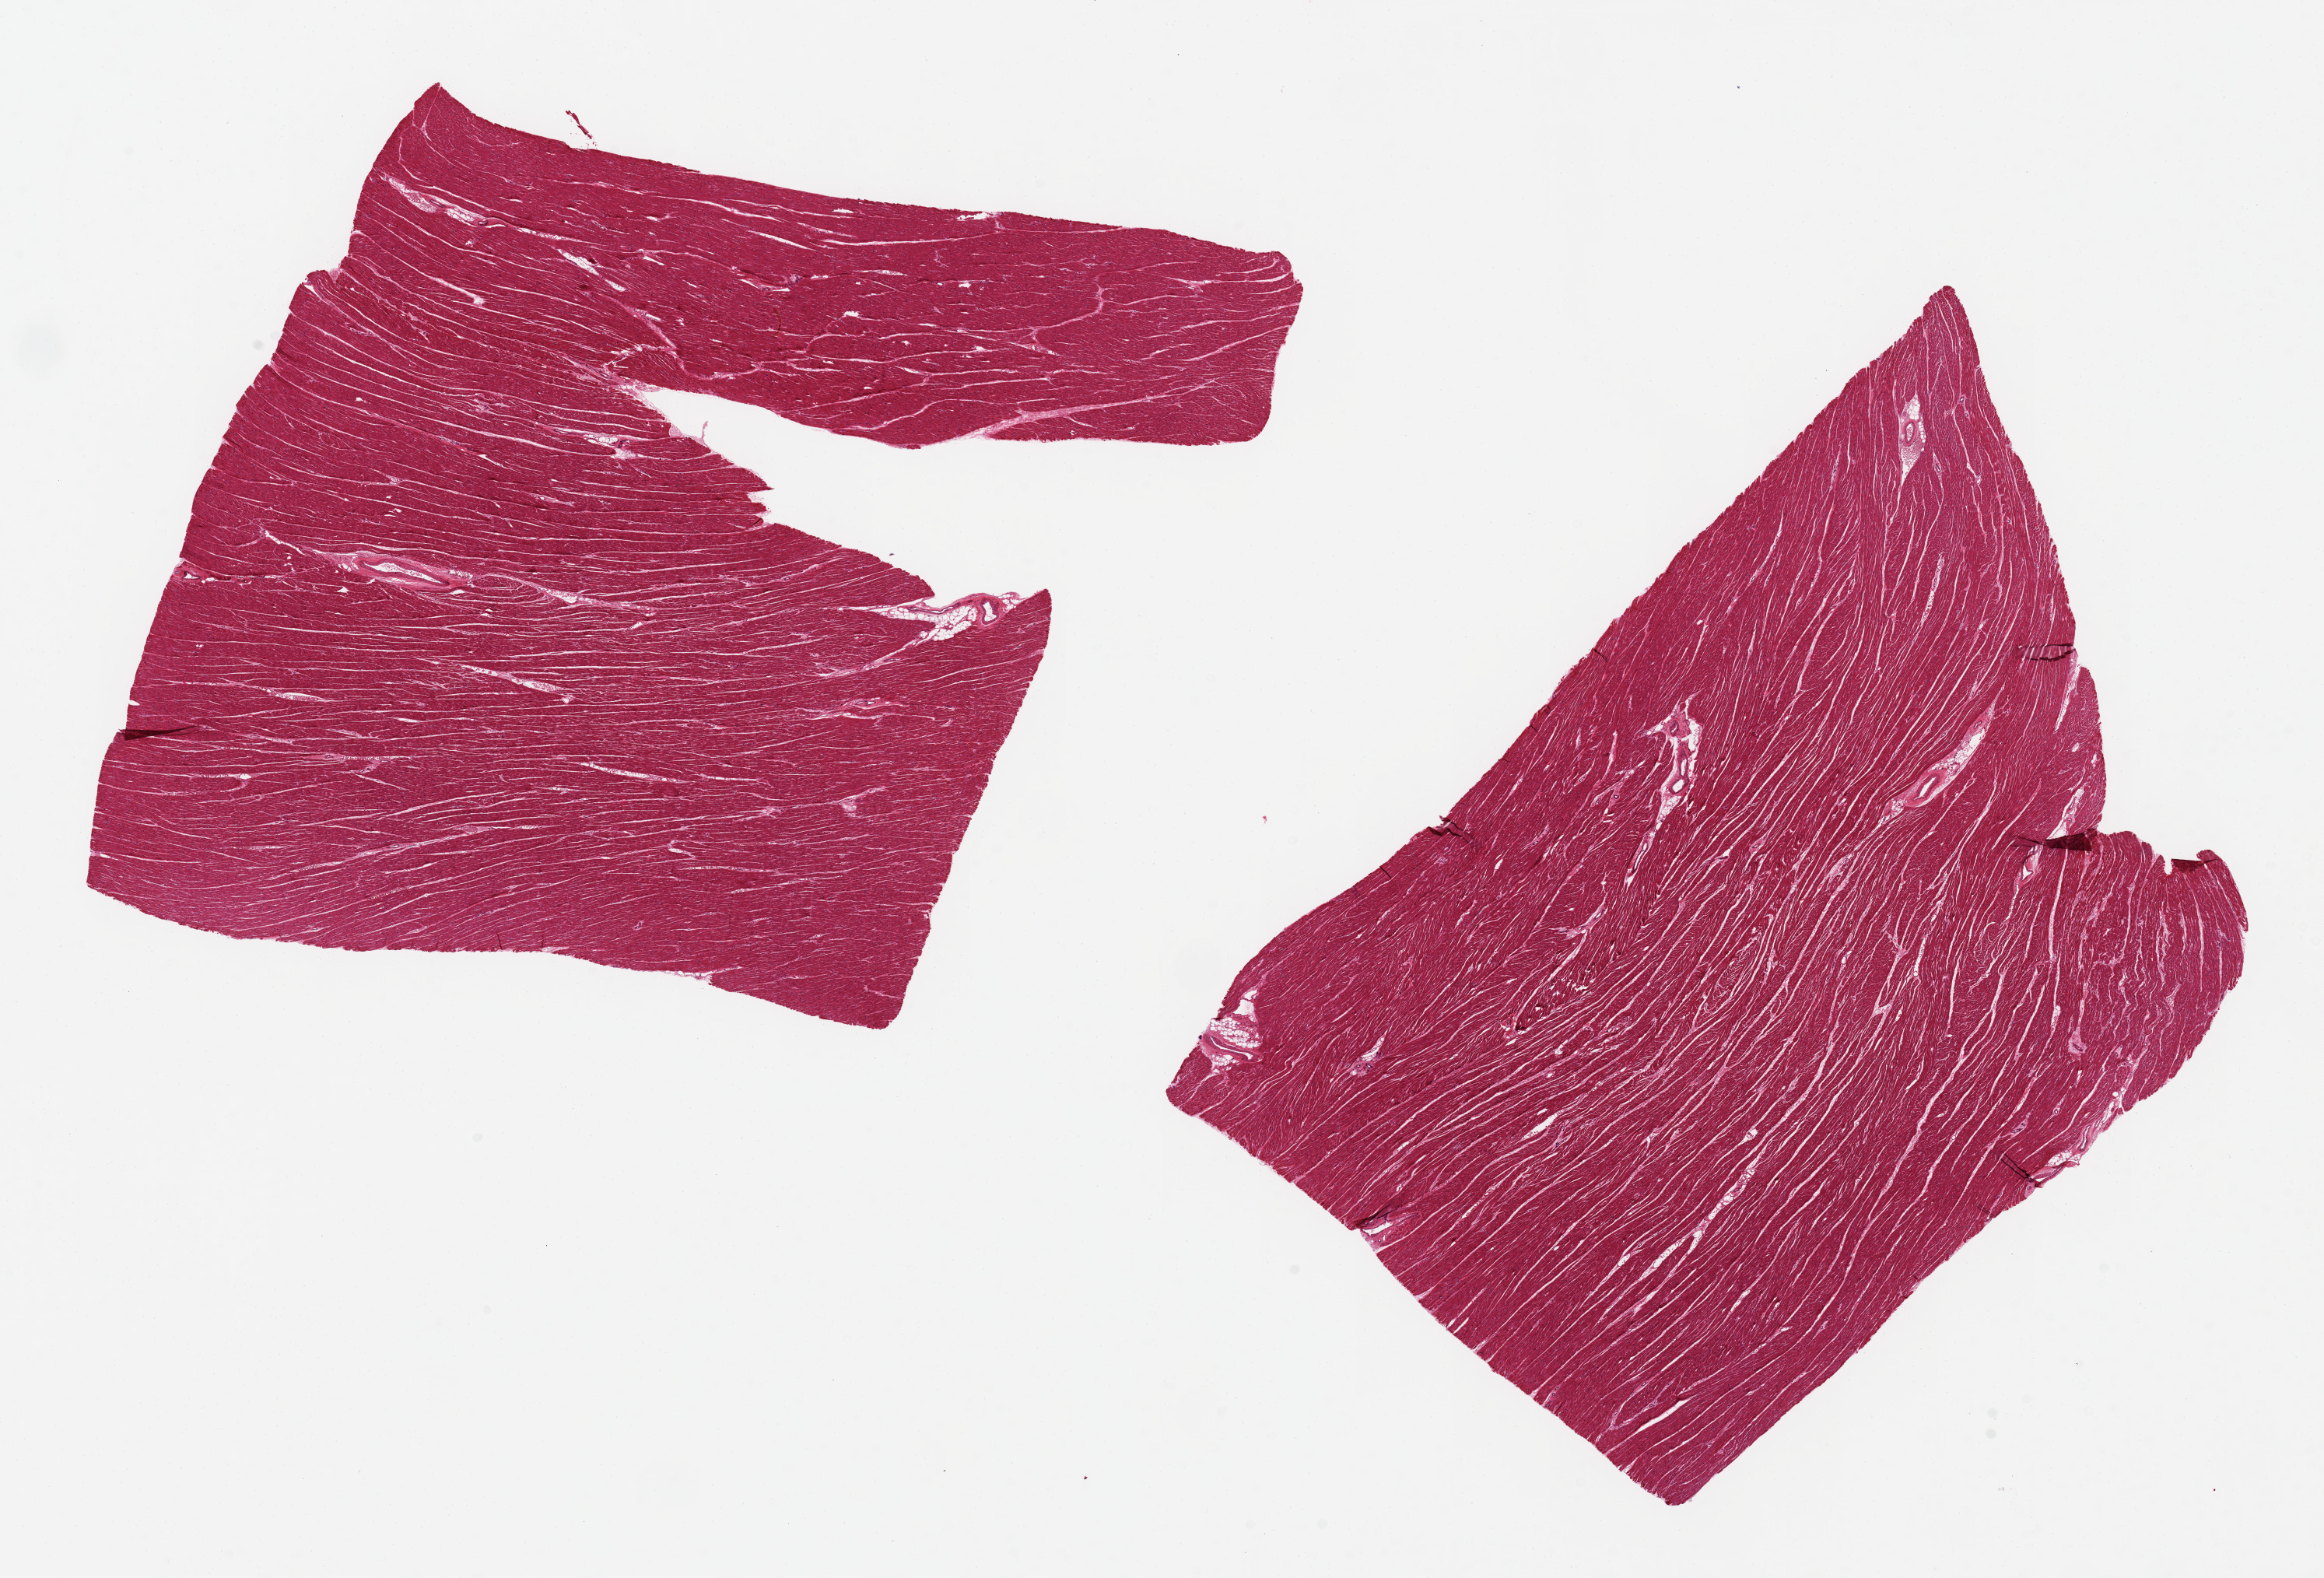
Whole-slide image, H&E stain, shown as a low-resolution overview of the whole scanned area (about 23.6 x 16.0 mm, from a 20x scan). PAXgene-fixed paraffin-embedded (PFPE) section. Target tissue: heart. Tissue donor sample. Donor sex: male.
Review note (as recorded): 2 pieces, 11x7 & 9x8.7; few contraction bands.